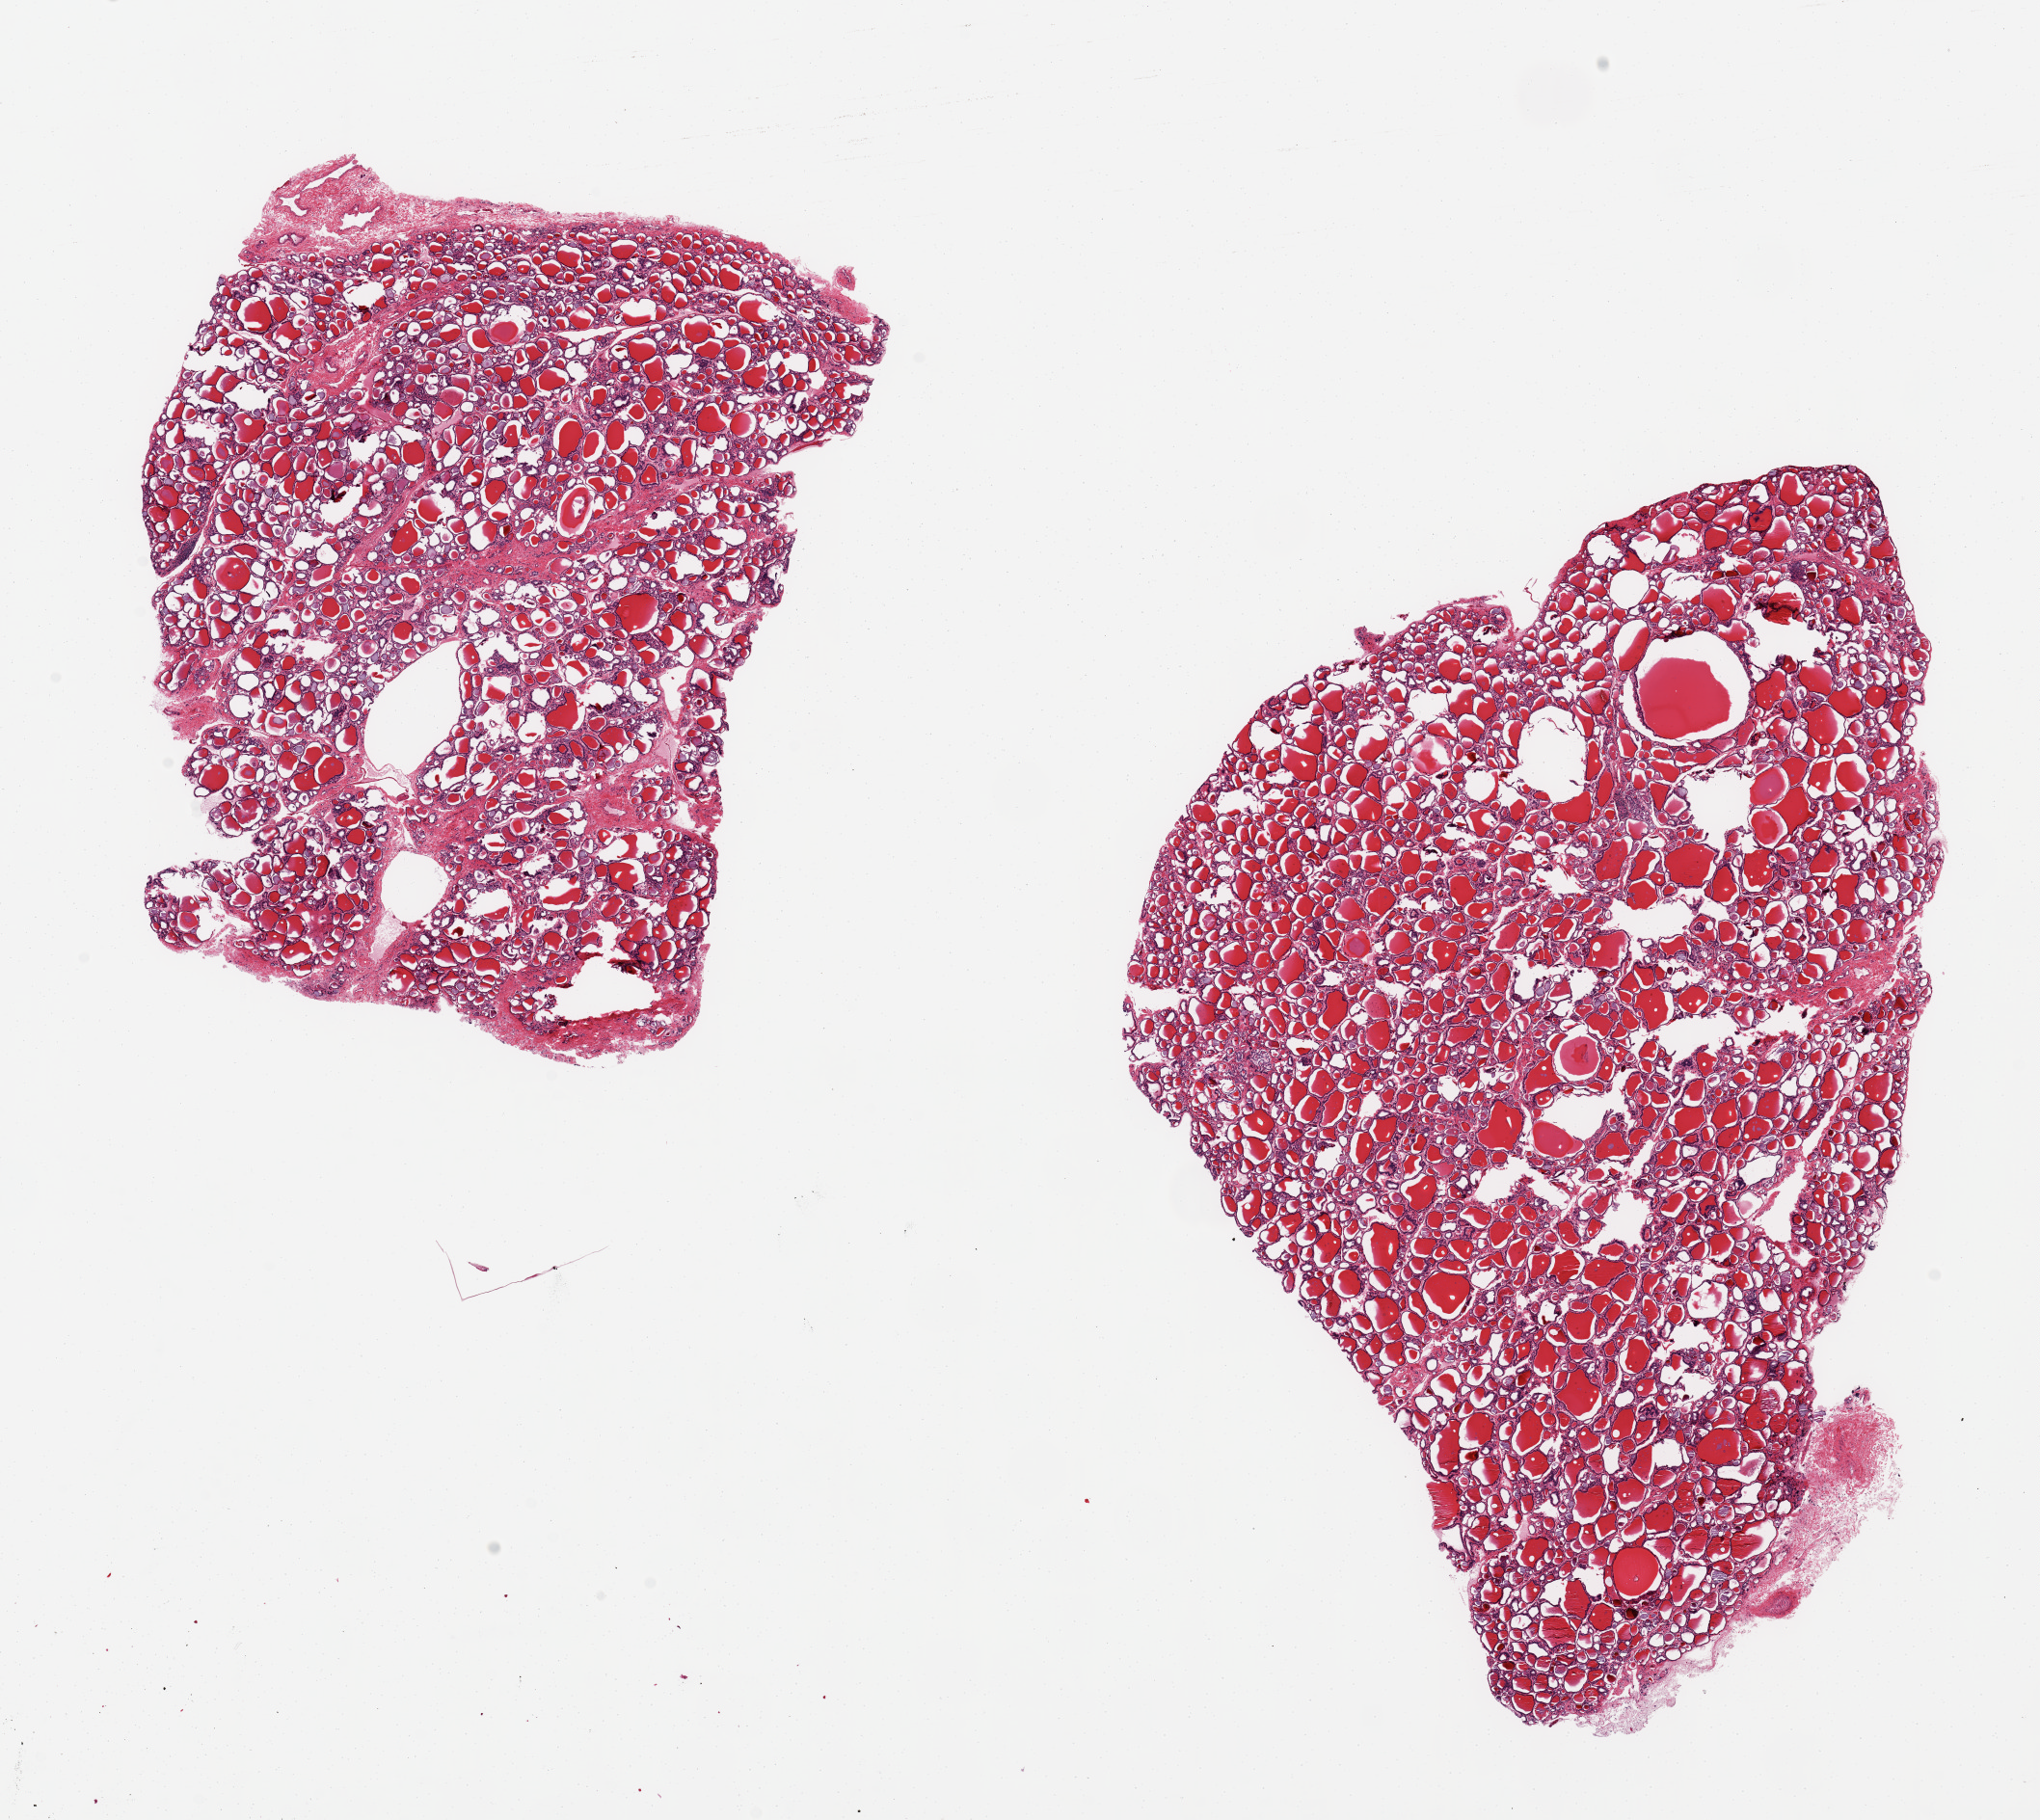
Digitized H&E-stained section, brightfield, shown as a low-resolution overview of the whole scanned area (about 16.7 x 14.9 mm, acquisition: 20x scan), PAXgene-fixed paraffin-embedded (PFPE) section, section of thyroid (target tissue), donor tissue sample. Donor: female.
Review note (as recorded): 2 pieces up to 10.5x6.5 mm.